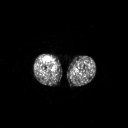
FDG PET of an extremity soft-tissue mass (from a PET/CT study), one axial slice; slice 249 of 311 in the series (ordered by position); 3.27 mm slice thickness; 128 × 128 image matrix, field of view 700 × 700 mm. Male patient, age 56 years. Case-level facts recorded for this patient, not image findings: histological type: pleiomorphic leiomyosarcoma; grade: intermediate; site of the primary tumour: right thigh.
Outlined on this slice (expert contour drawn on MRI and transferred to this co-registered scan by the dataset authors):
- gross tumour volume including surrounding oedema: bounding box <43,56,51,62> (left, top, right, bottom; pixels)